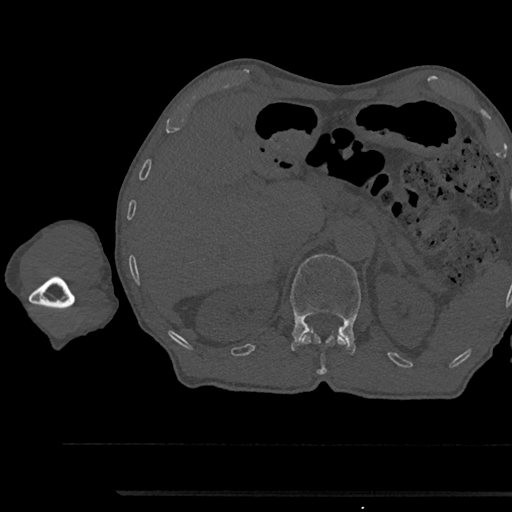
CT including the spine, one axial slice. Position 670 of 797 along the scan axis. Bone window (W 1800 / L 400 HU). 0.5 mm slice thickness. 512 × 512 image matrix. Patient: male, 79 years. From the clinical record (not read from this slice): primary cancer: prostate.
Annotated regions visible in this slice (semi-automatically segmented with operator editing):
- L1 vertebra: bounding box [x1, y1, x2, y2] px = [290, 254, 361, 354]
- T12 vertebra: [300, 330, 350, 374]